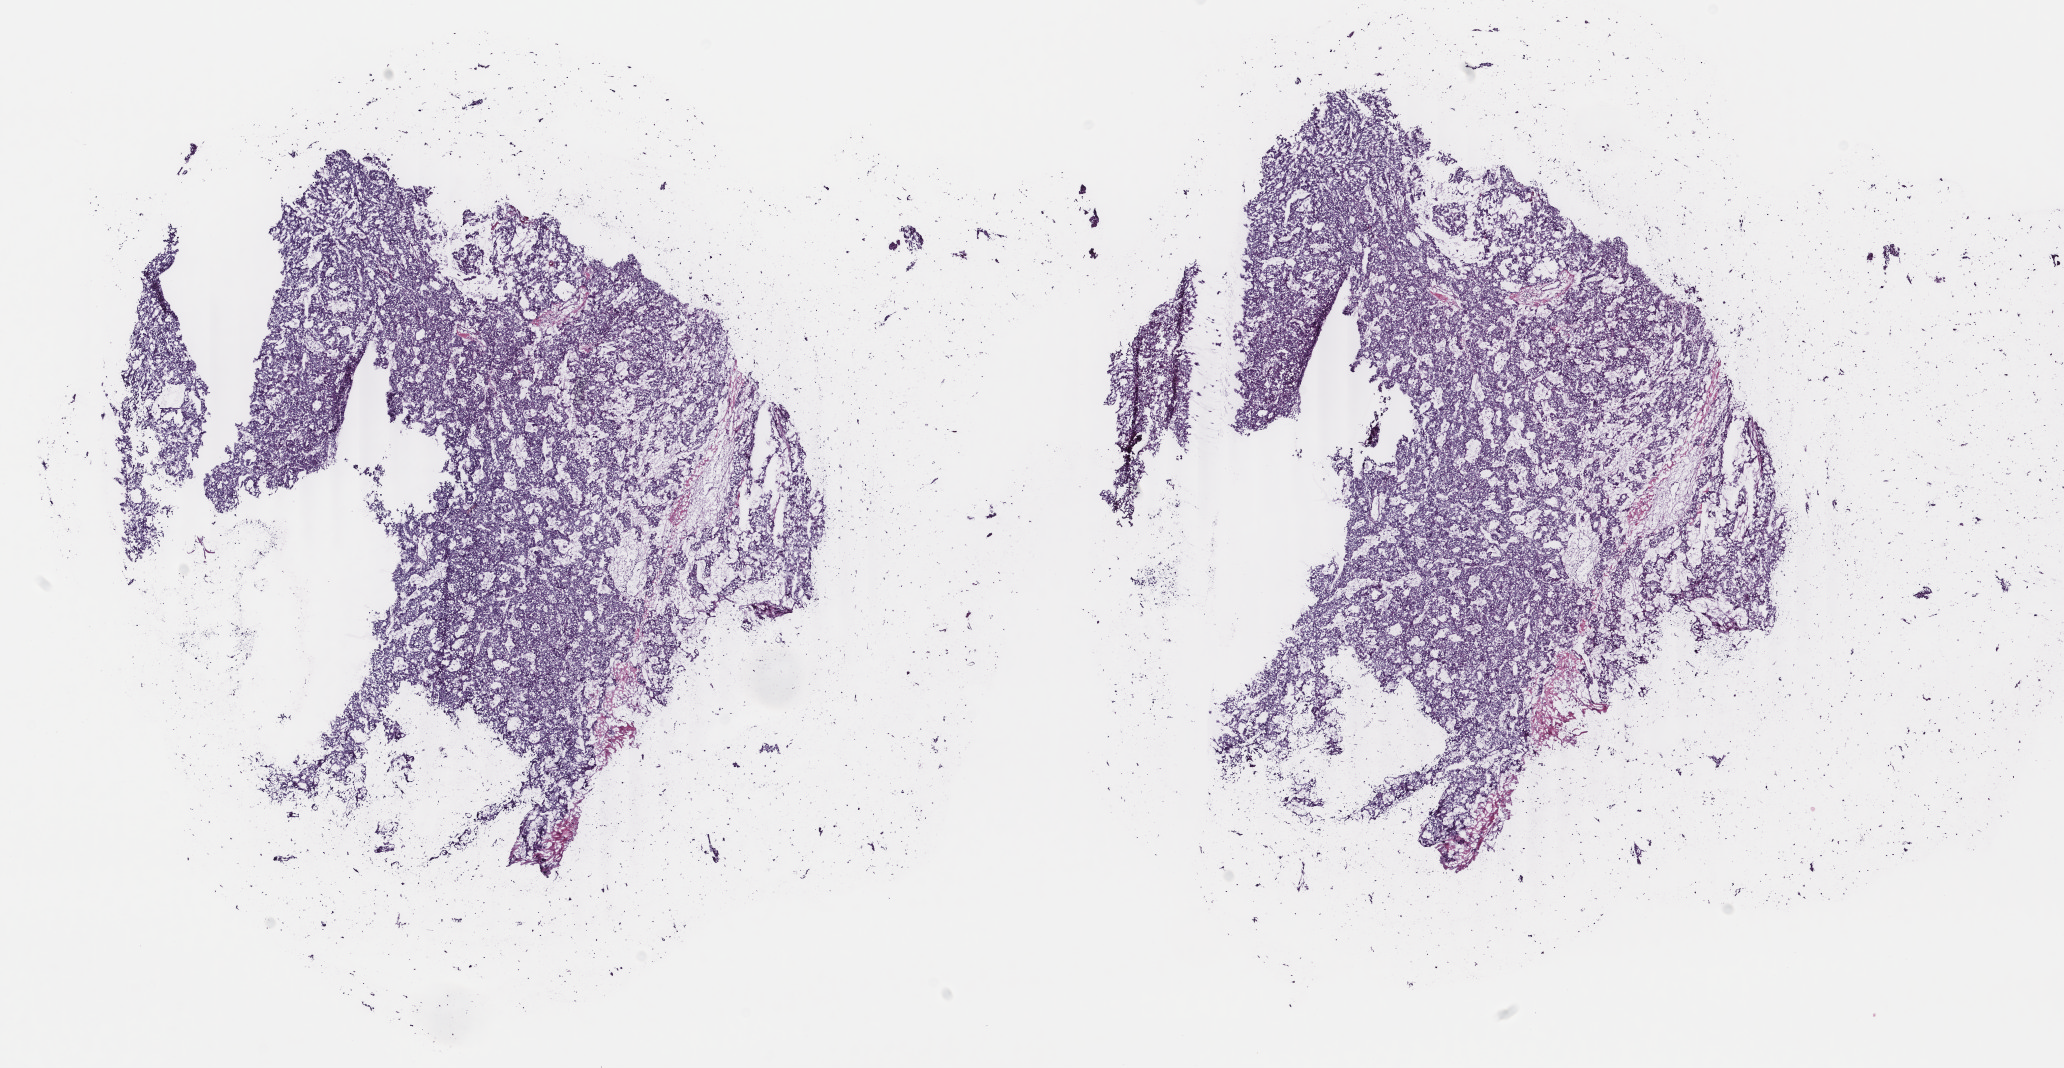
Whole-slide histology image, H&E — shown as a low-resolution overview of the whole scanned area (about 16.4 x 8.5 mm, slide scanned at 40x), frozen section from the top of the tissue portion, primary tumour sample from the liver. Patient: male, age at initial diagnosis 69 years. Histologic grade: G3 (poorly differentiated). Pathologist review of this section (percent, as recorded): tumour cells 80%, tumour nuclei 80%, normal cells 0%, stromal cells 20%, necrosis 0%. Infiltration values recorded for this section: lymphocyte infiltration 2%, monocyte infiltration 2%, neutrophil infiltration 0%.
AJCC pathologic stage: I (6th edition). Diagnosis: Hepatocellular carcinoma, NOS.